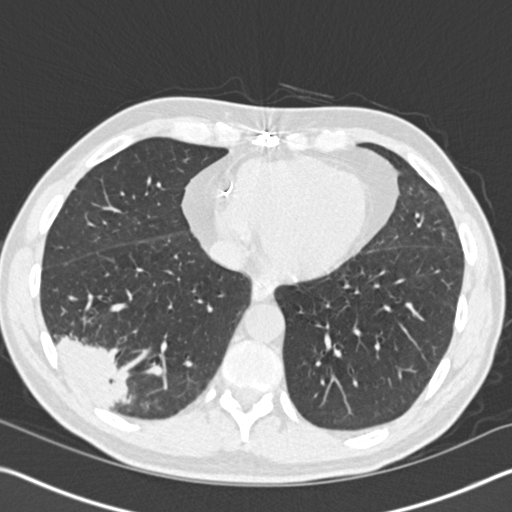
Axial slice from a low-dose chest CT screening exam; first (baseline) screen; lung window (W 1500 / L -600 HU); 2 mm slice thickness; 120 kVp; slice 109 of 161 in the series; 512 × 512 image matrix. Male participant, aged 61 years at enrolment.
• Lesion marked by an expert reader, box from (x=30, y=302) to (x=148, y=420) px.
• The exam's reader record, not a measurement of the box and not confirmed to be the same lesion: non-calcified nodule or mass ≥4 mm, right lower lobe, 52 × 36 mm, spiculated (stellate) margins, soft tissue attenuation.
• Official screen result: positive, change unspecified: nodule(s) >= 4 mm or enlarging nodule(s), mass(es), or other non-specific abnormalities suspicious for lung cancer.
• Lung cancer was diagnosed 392 days after this screen (after the second annual screen): bronchiolo-alveolar adenocarcinoma, NOS, right lower lobe, moderately differentiated (G2), stage IIIB (AJCC 6th edition), 90 mm at pathology.